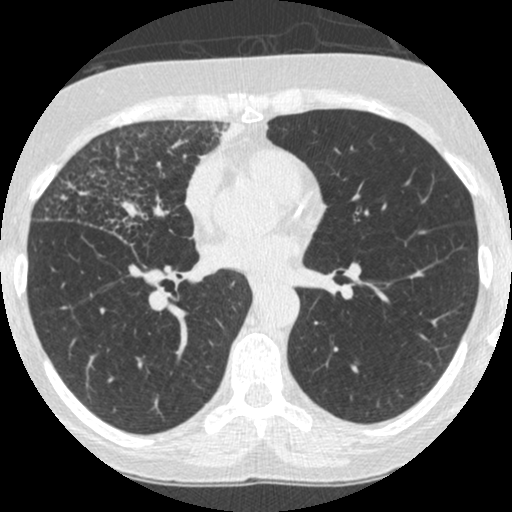
Low-dose screening chest CT, one axial slice; slice 127 of 253 in the series (ordered by position); reconstruction kernel STANDARD; 120 kVp; lung window (W 1500 / L -600 HU); 1.25 mm slice thickness; 512 × 512 image matrix, field of view 294 × 294 mm.
Structures marked on this image (outlined manually by an expert reader):
- lesion 4 (tumor, upper lobe of right lung): bounding box <201,119,242,157> (left, top, right, bottom; pixels)